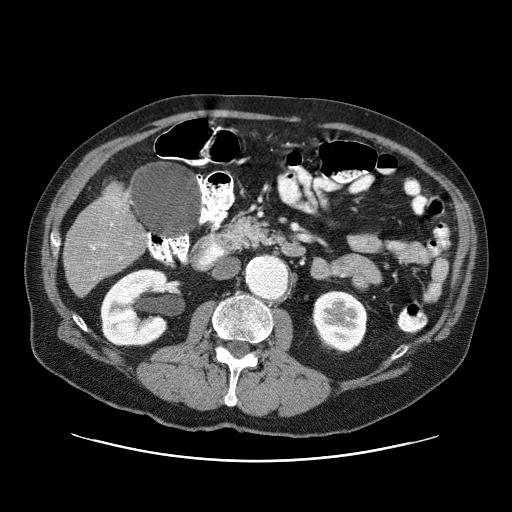
Contrast-enhanced abdominal CT (liver protocol), one axial slice; slice 16 of 87 in the series (ordered by position); reconstruction kernel STANDARD; one of 3 acquisitions stored at this slice position; soft-tissue window (W 400 / L 40 HU); 512 × 512 image matrix. From the clinical record (not read from this slice): diagnosis: hepatocellular carcinoma (patient treated with transarterial chemoembolisation; whether this scan precedes or follows treatment is not stated here); TNM stage (as recorded): Stage-IIIA; Child-Pugh class: A; tumour differentiation: well differentiated; tumour nodularity: multinodular.
Annotated regions visible in this slice (semi-automatic segmentation, software-assisted and operator-edited):
- liver parenchyma outside the tumour (the mass and vessels are separate outlines, so this box may not span the whole liver): box from (x=62, y=187) to (x=142, y=296) px
- mass: (x=102, y=182)–(x=127, y=208)
- liver vessels: (x=91, y=223)–(x=122, y=259)